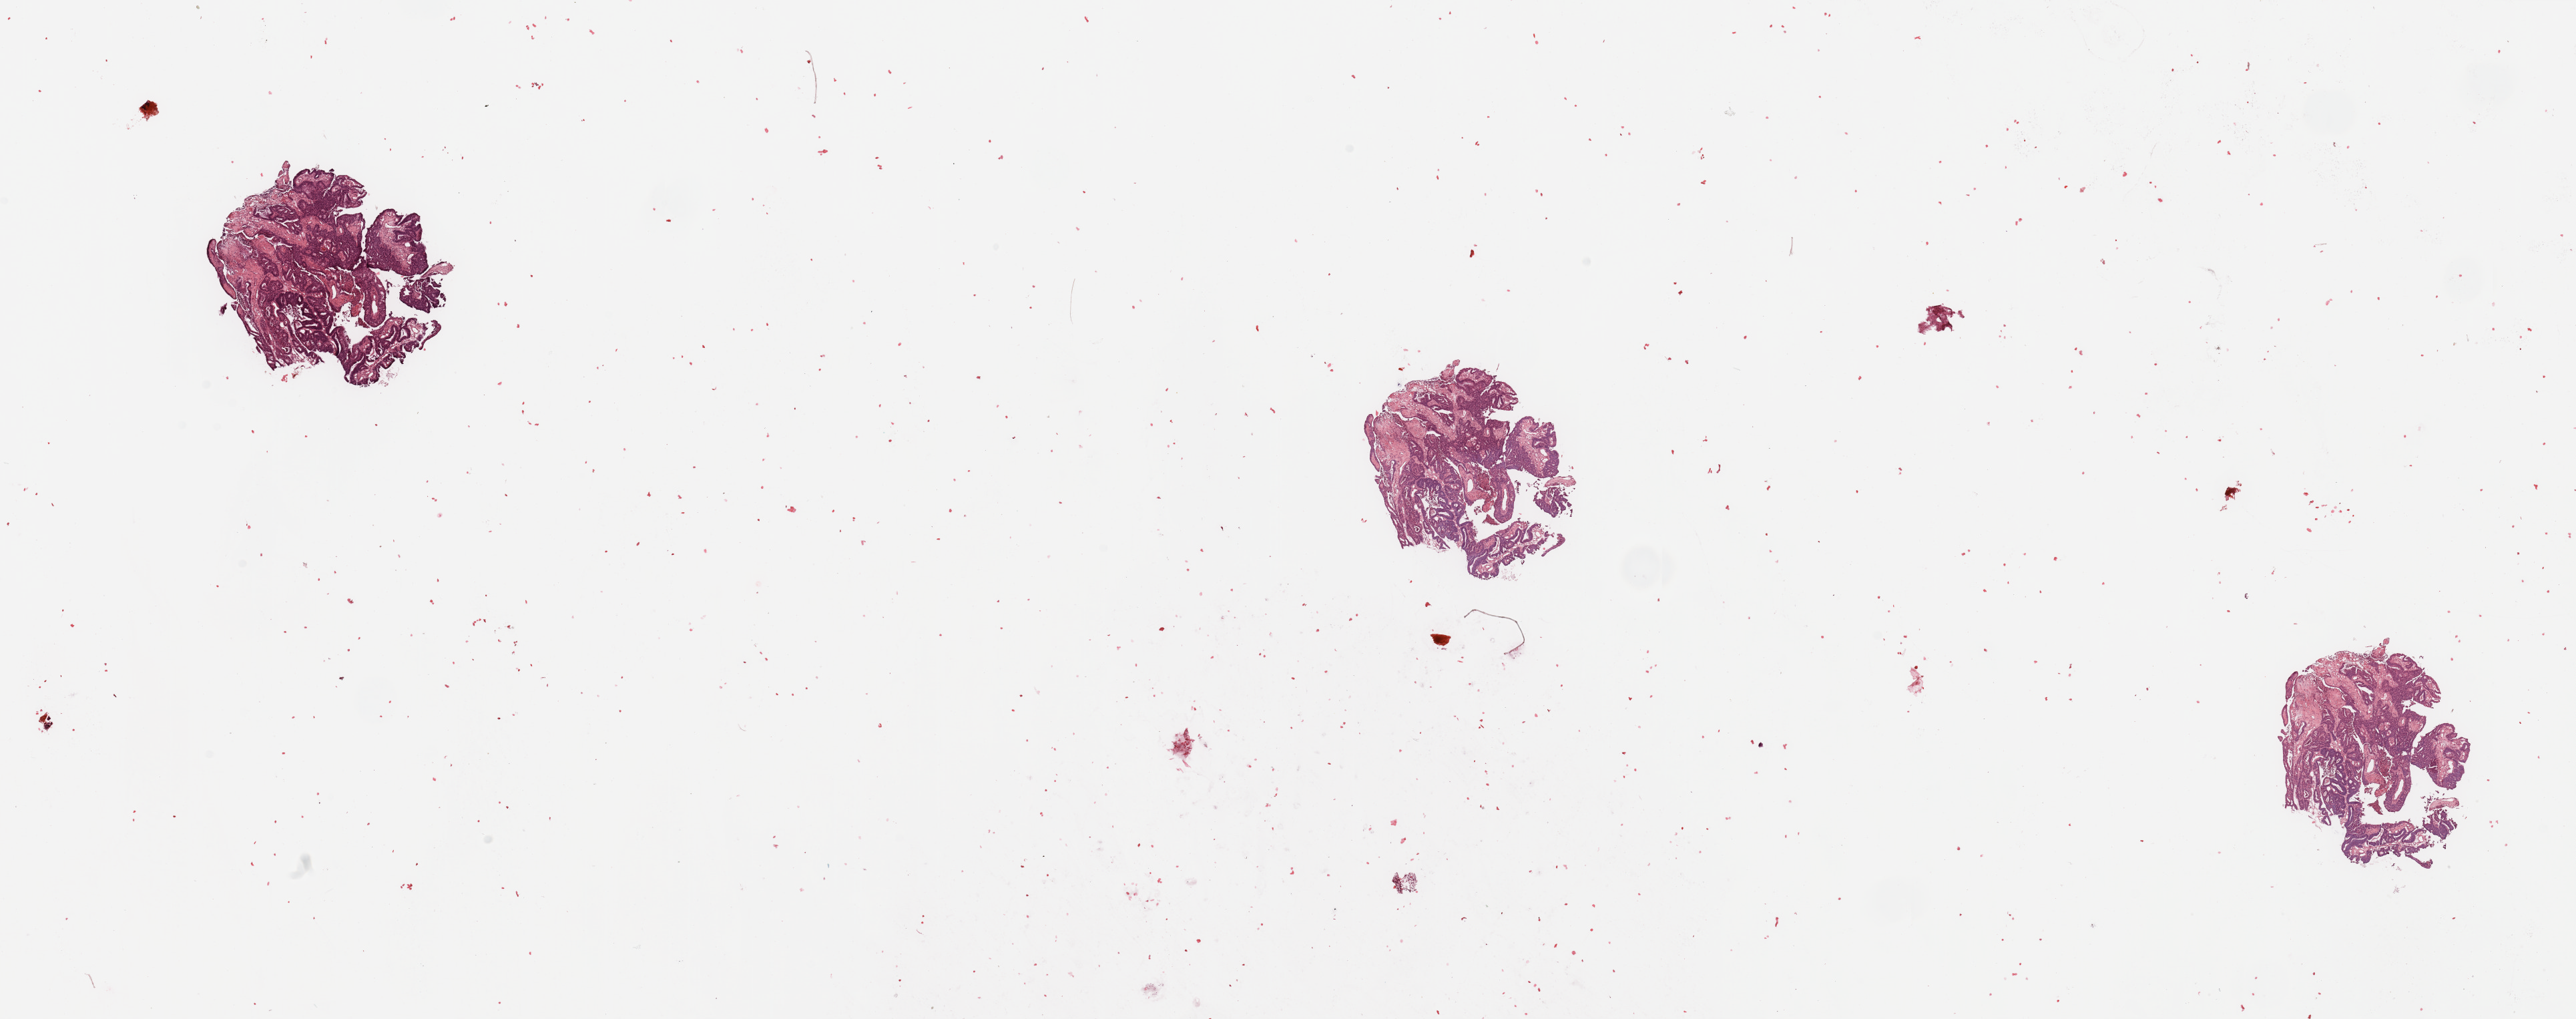
Hematoxylin and eosin (H&E) stained whole-slide image — low-resolution overview of the scanned area, about 30.5 x 12.1 mm (acquisition: 20x scan). Uterus, tumour tissue. 69-year-old female patient.
• primary tumour site (as recorded): anterior endometrium
• patient diagnosis (cohort enrolment): corpus endometrial carcinoma (uterus)